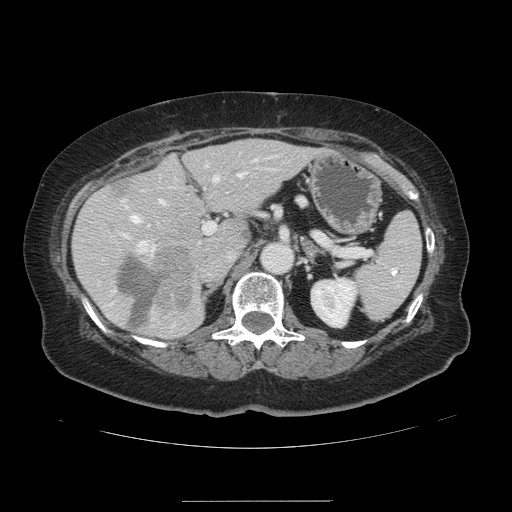
Contrast-enhanced abdominal CT, one axial slice. Slice 77 of 141 in the series (ordered by position). 120 kVp. Intravenous contrast given. Soft-tissue window (W 400 / L 40 HU). 512 × 512 image matrix. Female patient, age 74 years. Case-level facts recorded for this patient, not image findings: diagnosis: colorectal cancer liver metastases, imaged before liver resection.
Outlined on this slice (expert manual segmentation):
- hepatic veins: bounding box <130,173,242,227> (left, top, right, bottom; pixels)
- liver: <74,140,318,339>
- planned liver remnant (the part of the liver to remain after resection): <75,140,318,339>
- portal vein (with intrahepatic branches): <122,158,257,253>
- liver metastasis: <106,182,136,202>
- liver metastasis: <118,259,166,331>
- liver metastasis: <158,246,195,310>